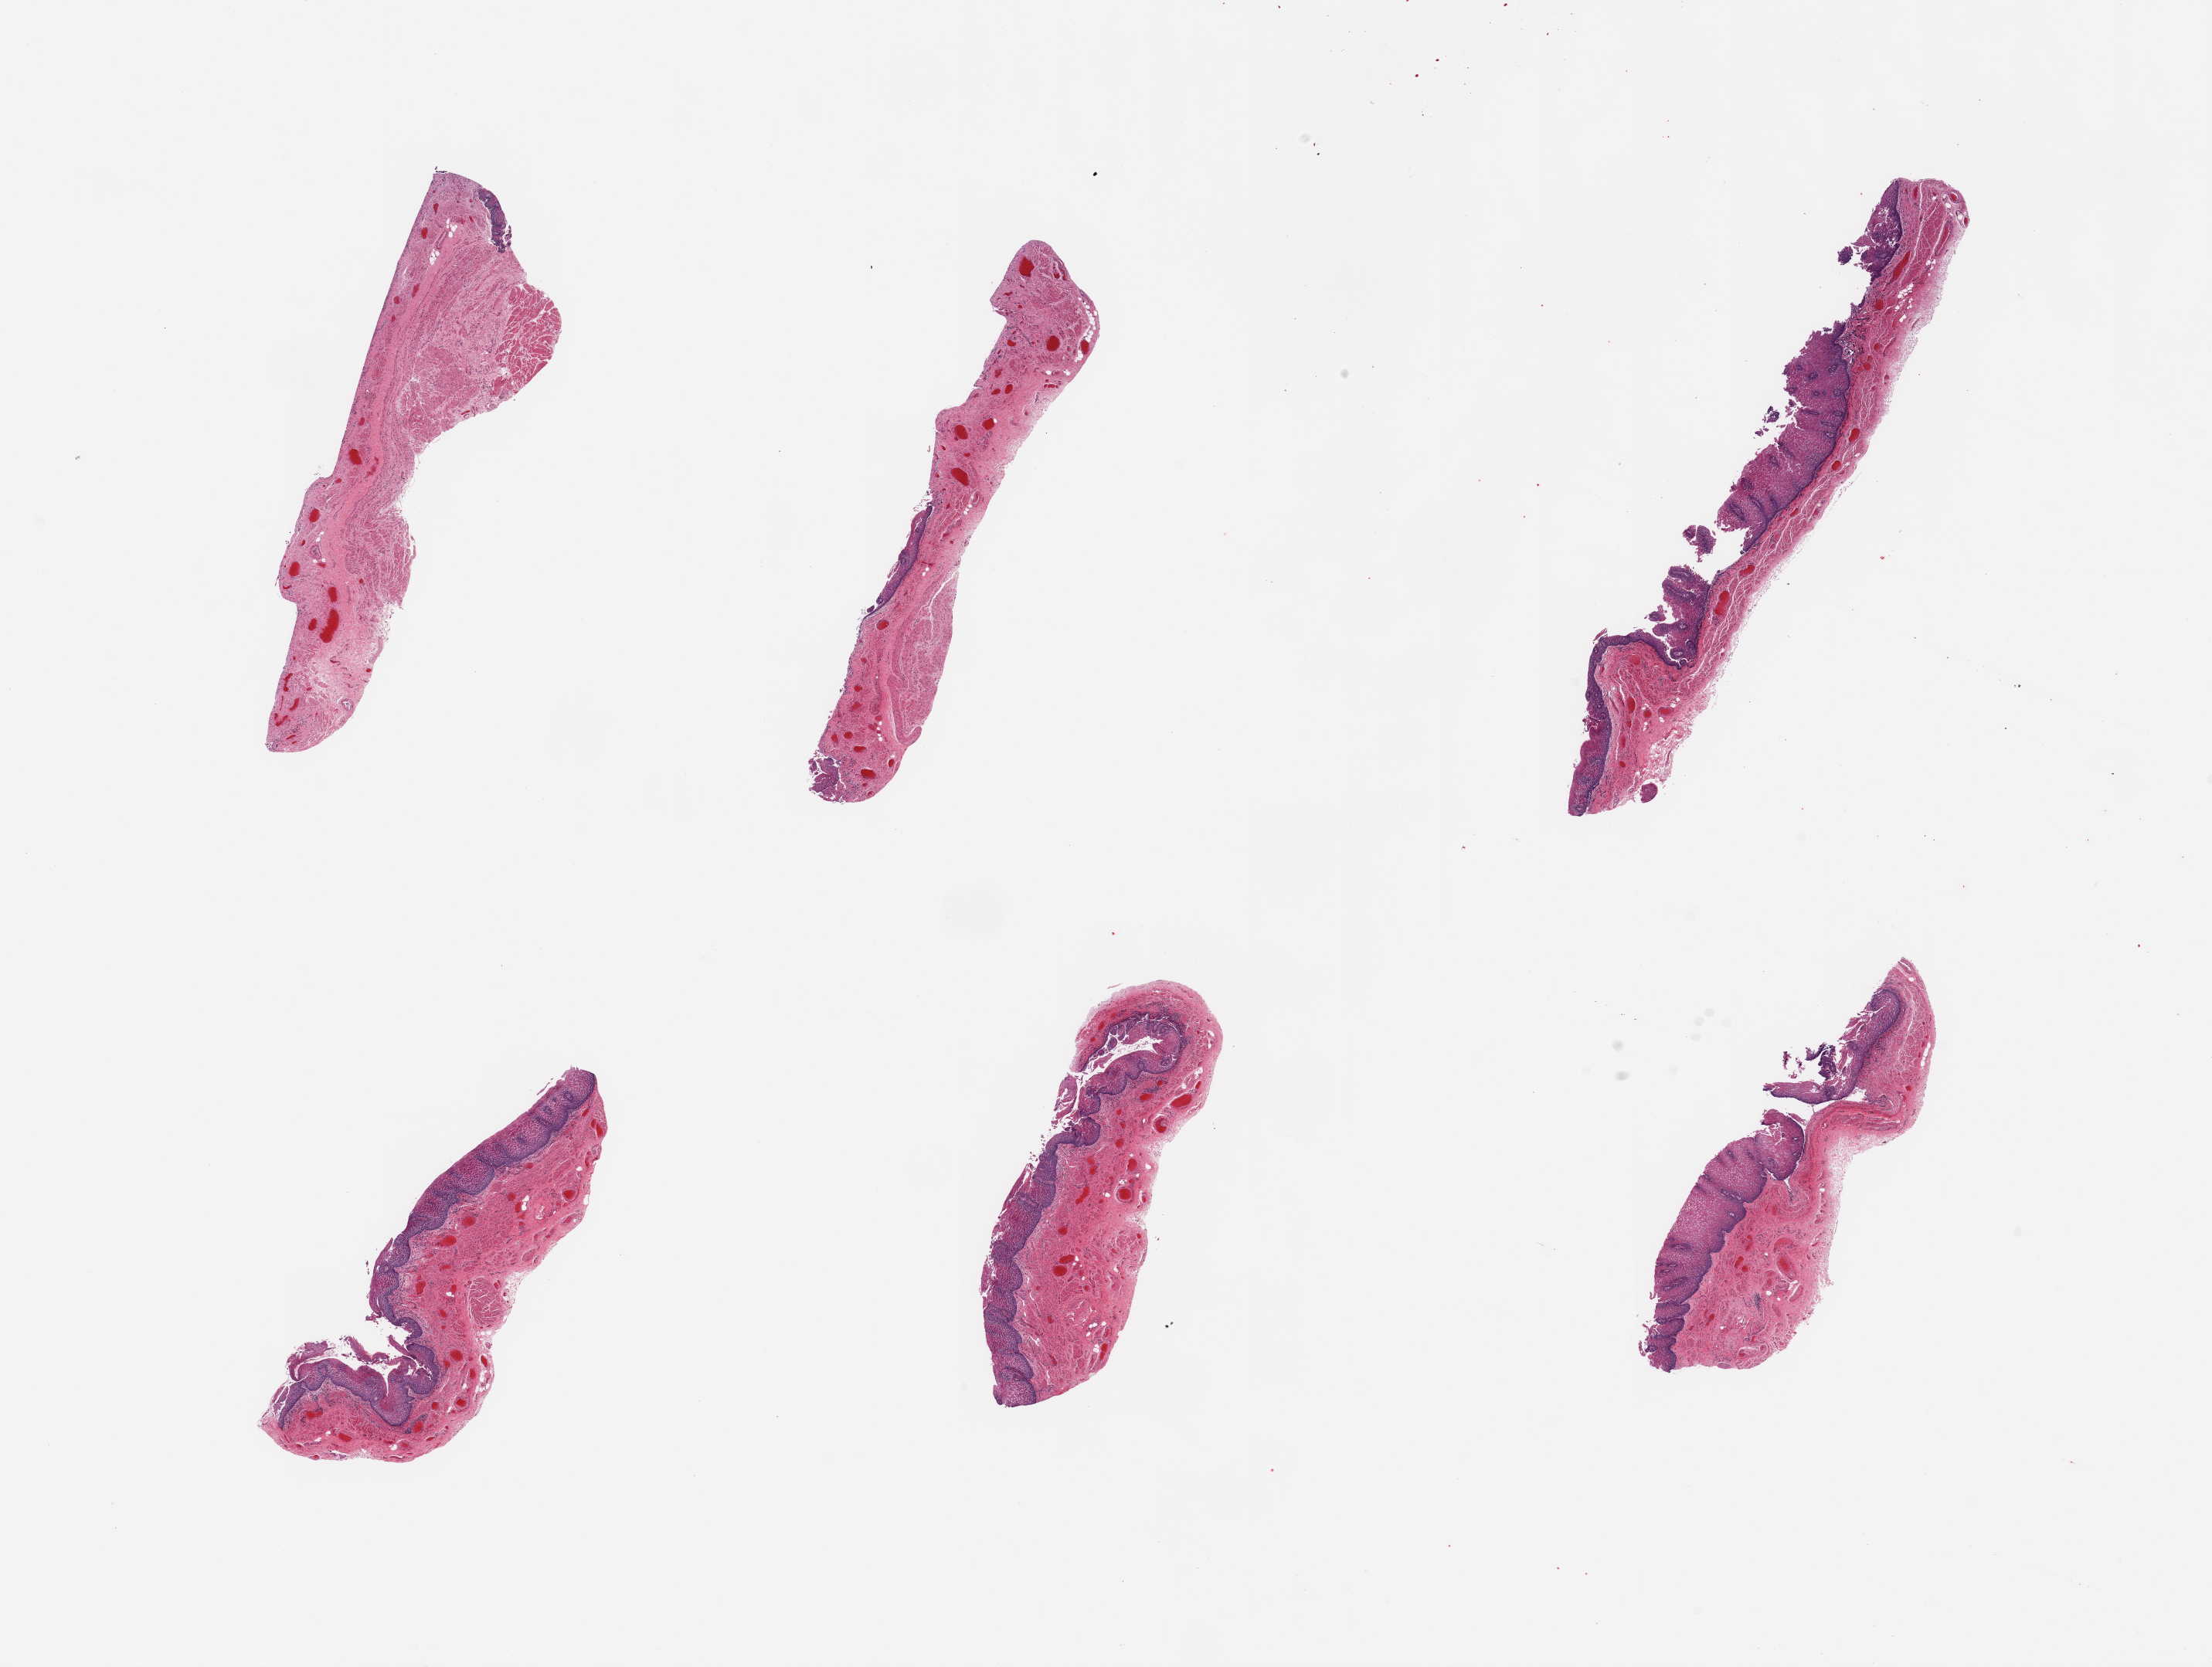
Whole-slide image, hematoxylin and eosin (H&E) stain, brightfield — whole scanned area (about 22.6 x 17.1 mm) shown as a low-resolution overview. PAXgene-fixed paraffin-embedded (PFPE) section. Sampled site (target tissue): esophageal mucous membrane. Donor tissue sample. Donor: male.
- pathologist's review note for this sample: 6 pieces ,squamous mucosa up to ~0.3mm, ~20% thickness, but variably sloughing, degenerating